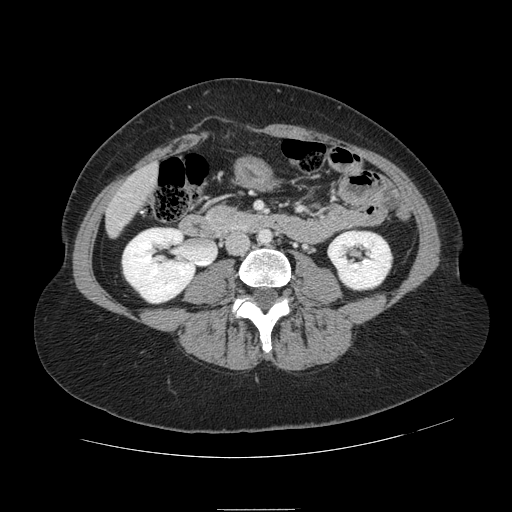
Contrast-enhanced abdominal CT, one axial slice. Position 9 of 121 along the scan axis. 120 kVp. Intravenous contrast given. Soft-tissue window (W 400 / L 40 HU). 2.5 mm slice thickness. 512 × 512 image matrix, field of view 400 × 400 mm. Female patient, age 52 years. Case-level facts recorded for this patient, not image findings: diagnosis: colorectal cancer liver metastases, imaged before liver resection; multiple liver metastases: yes; largest metastasis: 6.3 cm; disease in both lobes: no.
Annotated regions visible in this slice (manually delineated by an expert):
- liver: bounding box (x1, y1, x2, y2) in pixels: (107, 166, 157, 235)